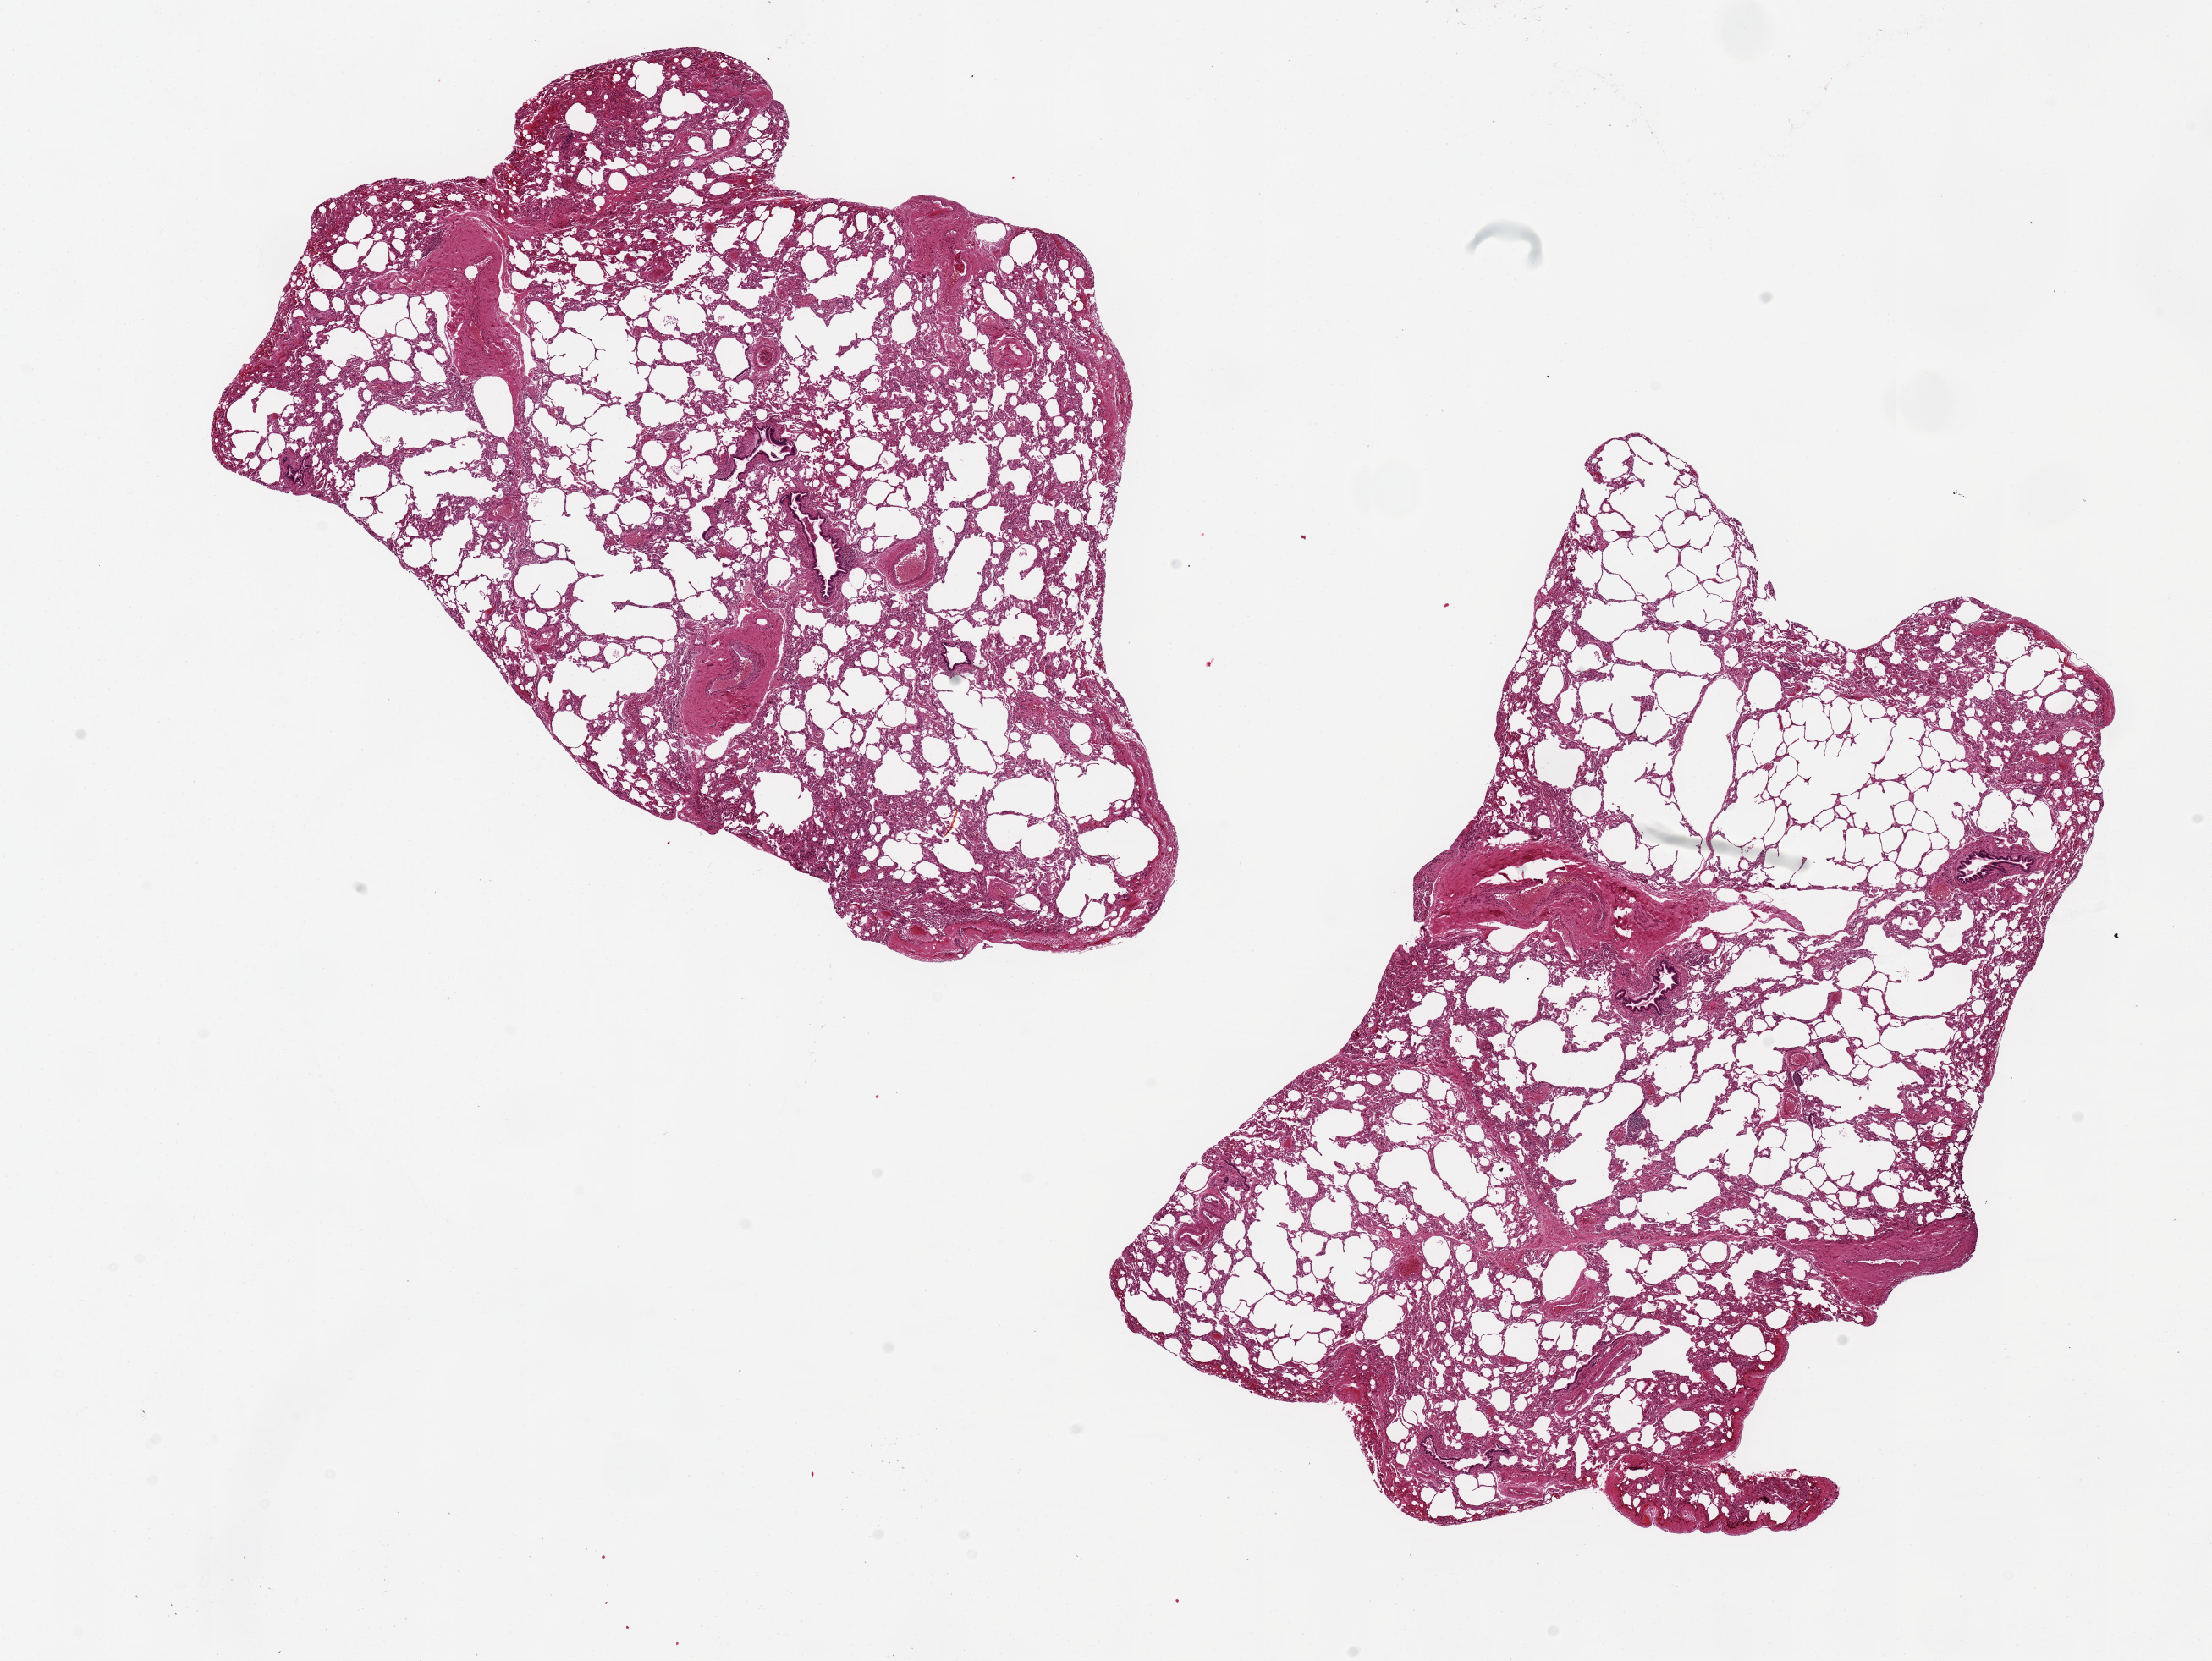
Whole-slide image, hematoxylin and eosin (H&E) stain, shown as a low-resolution overview of the whole scanned area (about 20.7 x 15.5 mm, from a 20x scan); PAXgene-fixed, paraffin-embedded tissue; sampled site (target tissue): lung; donor tissue sample. Donor: male.
Pathologist's review note for this sample: 2 aliquots, ~9x6mm. Fairly well preserved, minimal congestion.